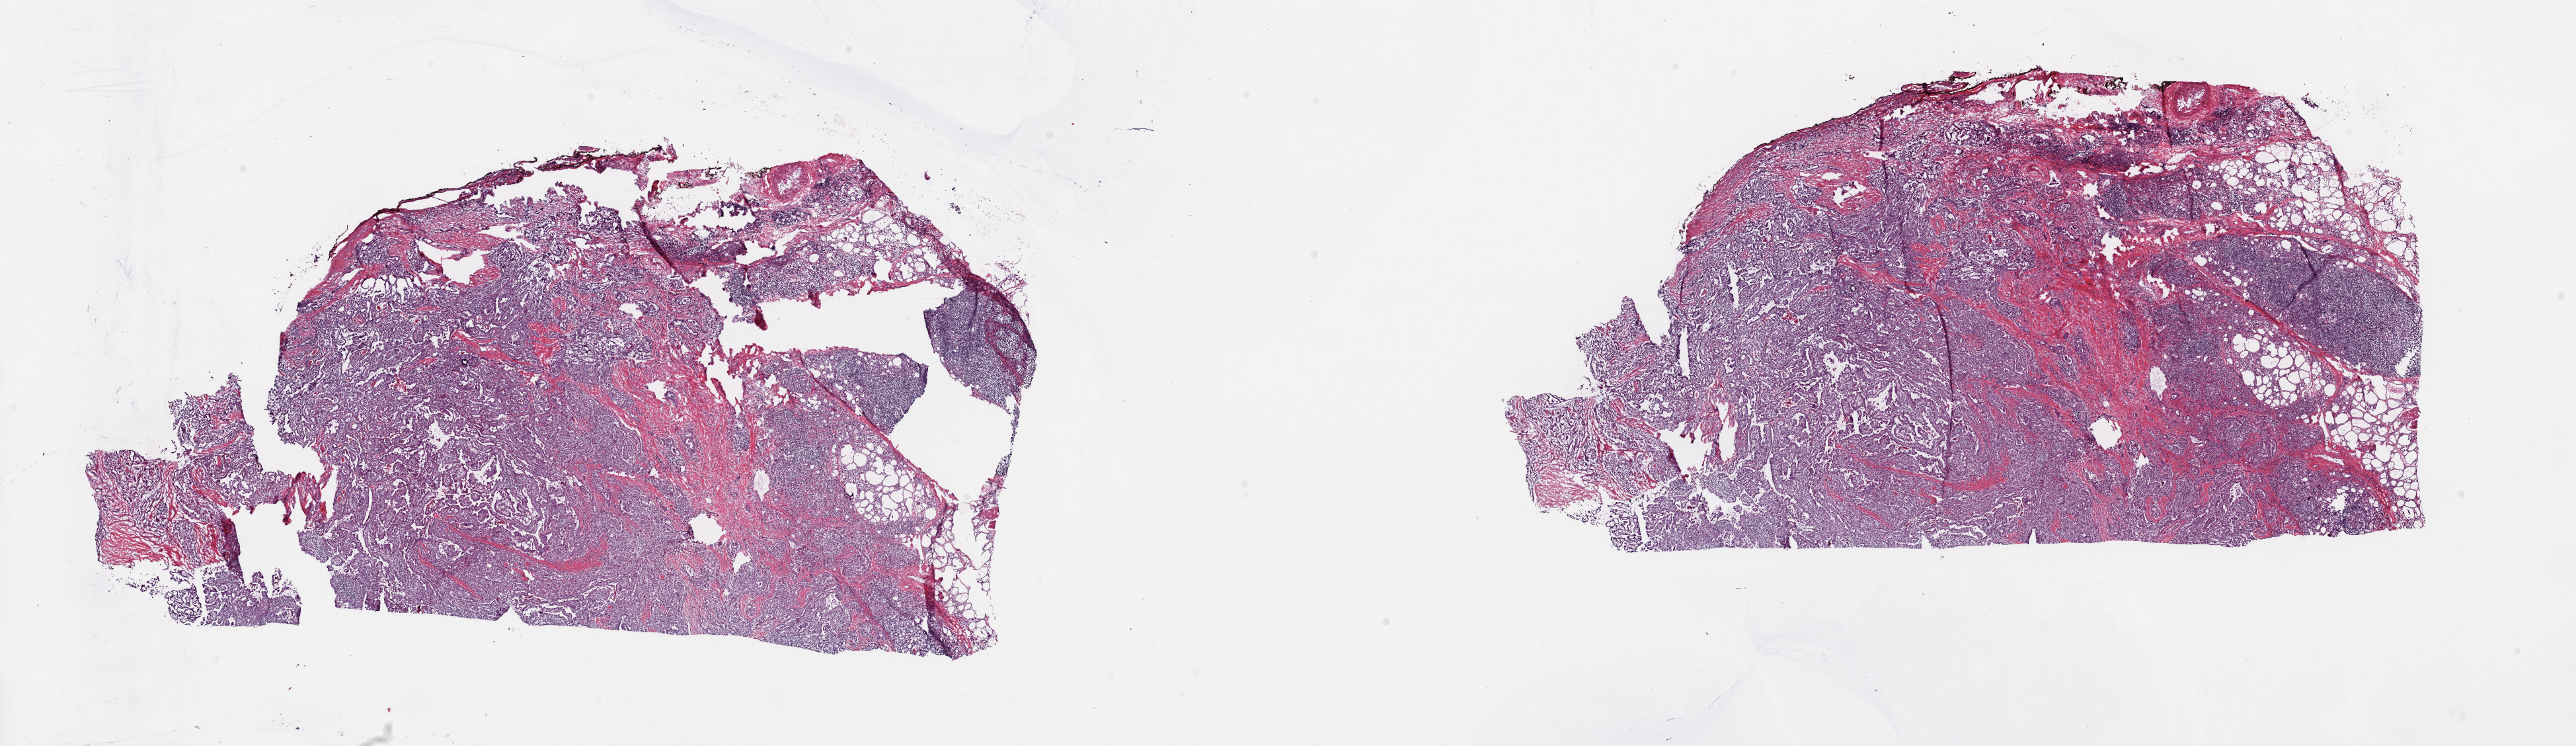
Whole-slide histology image, H&E-stained, low-resolution overview of the scanned area, about 30.8 x 8.9 mm (from a 40x scan); frozen section; sample: primary tumour, thyroid. Female, age 69 years at initial diagnosis.
Pathologic diagnosis: Papillary adenocarcinoma, NOS.